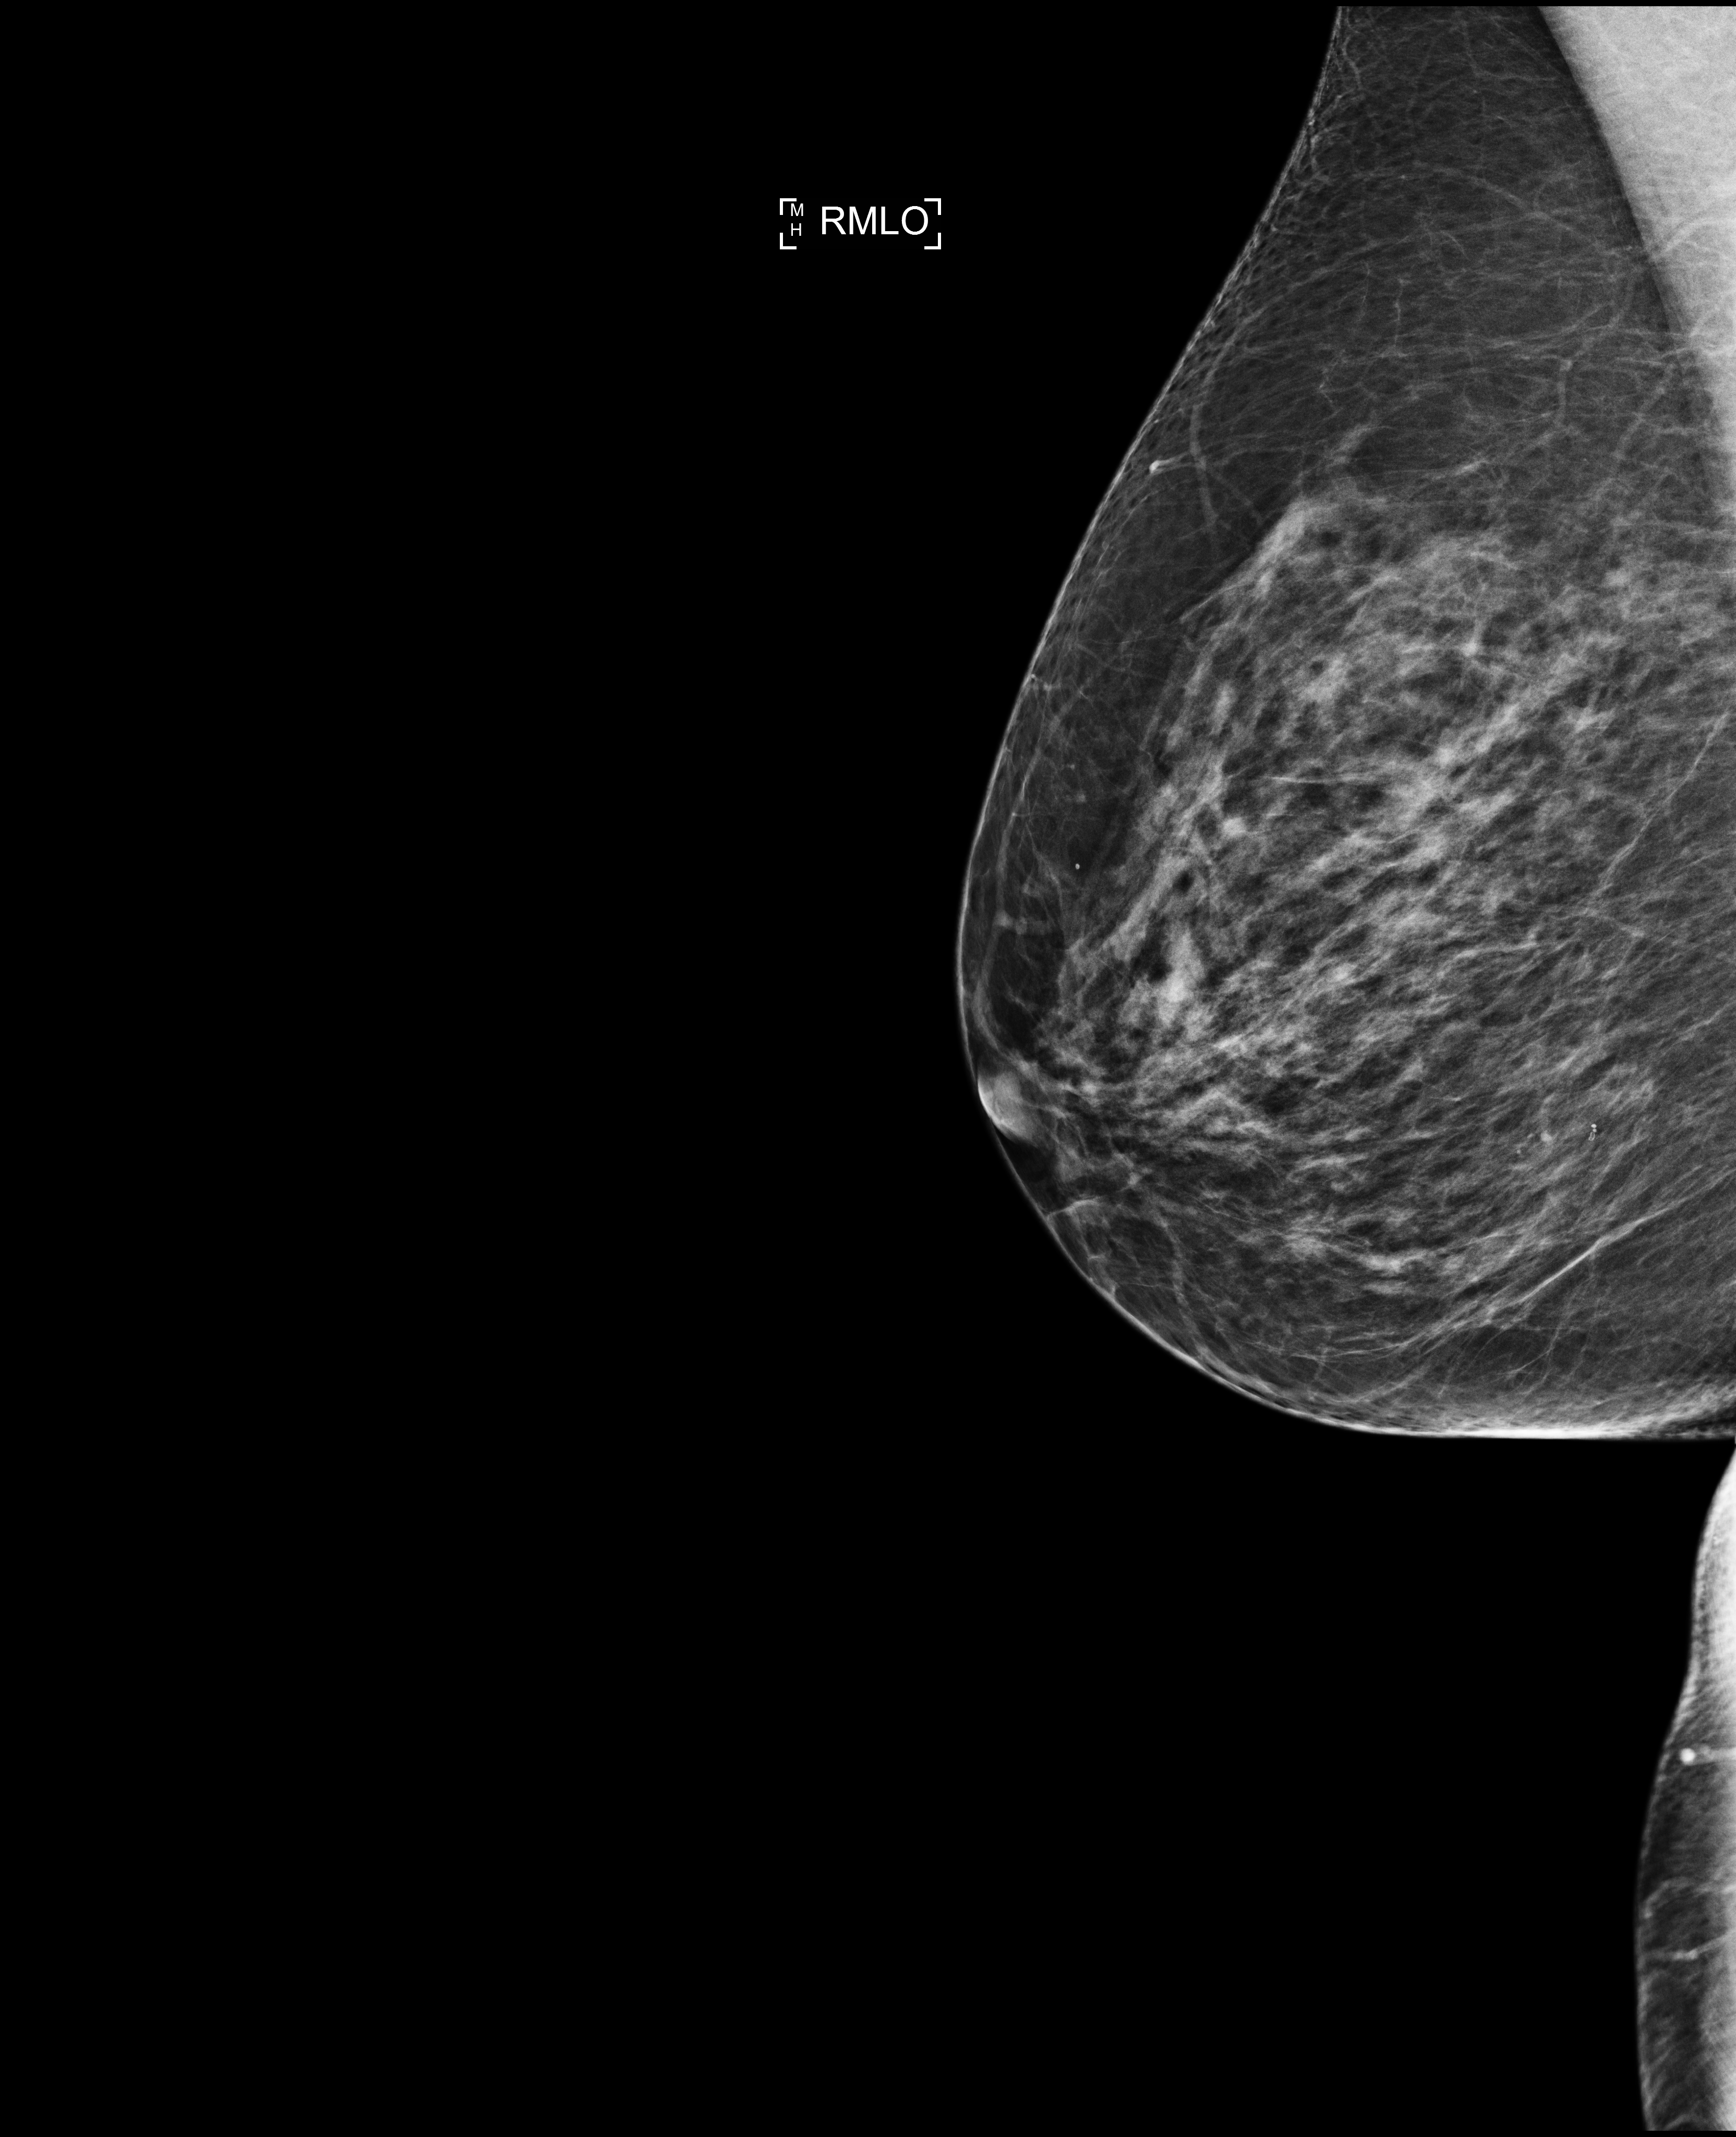
Full-field digital mammogram (FFDM), right breast, MLO view, screening examination. Patient aged 70 years (female).
BI-RADS breast density category at the screening exam (both breasts, scale 1–4): 2. Final BI-RADS category for the screening round (tomosynthesis exam, both breasts): category 1. Recall: no recall after this screen.